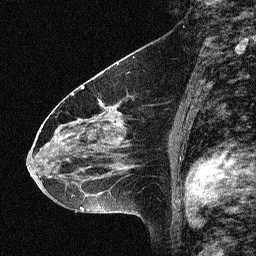
Breast MRI (dynamic contrast-enhanced), one sagittal slice. Position 34 of 64 along the scan axis. Dynamic contrast-enhanced study with each time point stored as its own series, time point 2 of 3 at this slice position (early post-contrast, ordered by acquisition time). 1.5 T. TE 4.5 ms, TR 11 ms. 2.06 mm slice thickness. 256 × 256 image matrix, field of view 200 × 200 mm. Patient: female, 46 years. Case-level facts recorded for this patient, not image findings: setting: breast cancer imaged before/during neoadjuvant chemotherapy; receptor status: HER2-positive.
Structures marked on this image (semi-automatic segmentation, software-assisted and operator-edited):
- analysis volume of interest (the breast-tissue region the enhancement analysis was run in; not a lesion): box from (x=42, y=80) to (x=150, y=180) px
- tumour enhancement mask (voxels above the 90 % enhancement threshold inside the analysis volume of interest): (x=45, y=87)–(x=119, y=153)